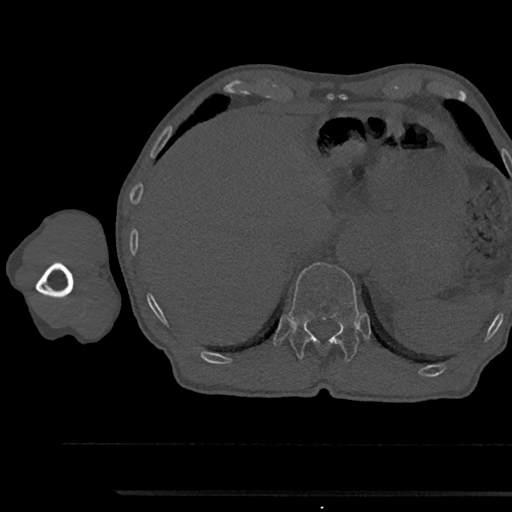
CT including the spine, one axial slice; slice 728 of 797 in the series (ordered by position); reconstruction kernel Br40s/3; 120 kVp; bone window (W 1800 / L 400 HU); 0.5 mm slice thickness; 512 × 512 image matrix, field of view 367 × 367 mm. Patient: male, 79 years. Case-level facts recorded for this patient, not image findings: primary cancer: prostate.
Outlined on this slice (semi-automatic segmentation, software-assisted and operator-edited):
- T12 vertebra: box from (x=288, y=261) to (x=360, y=361) px